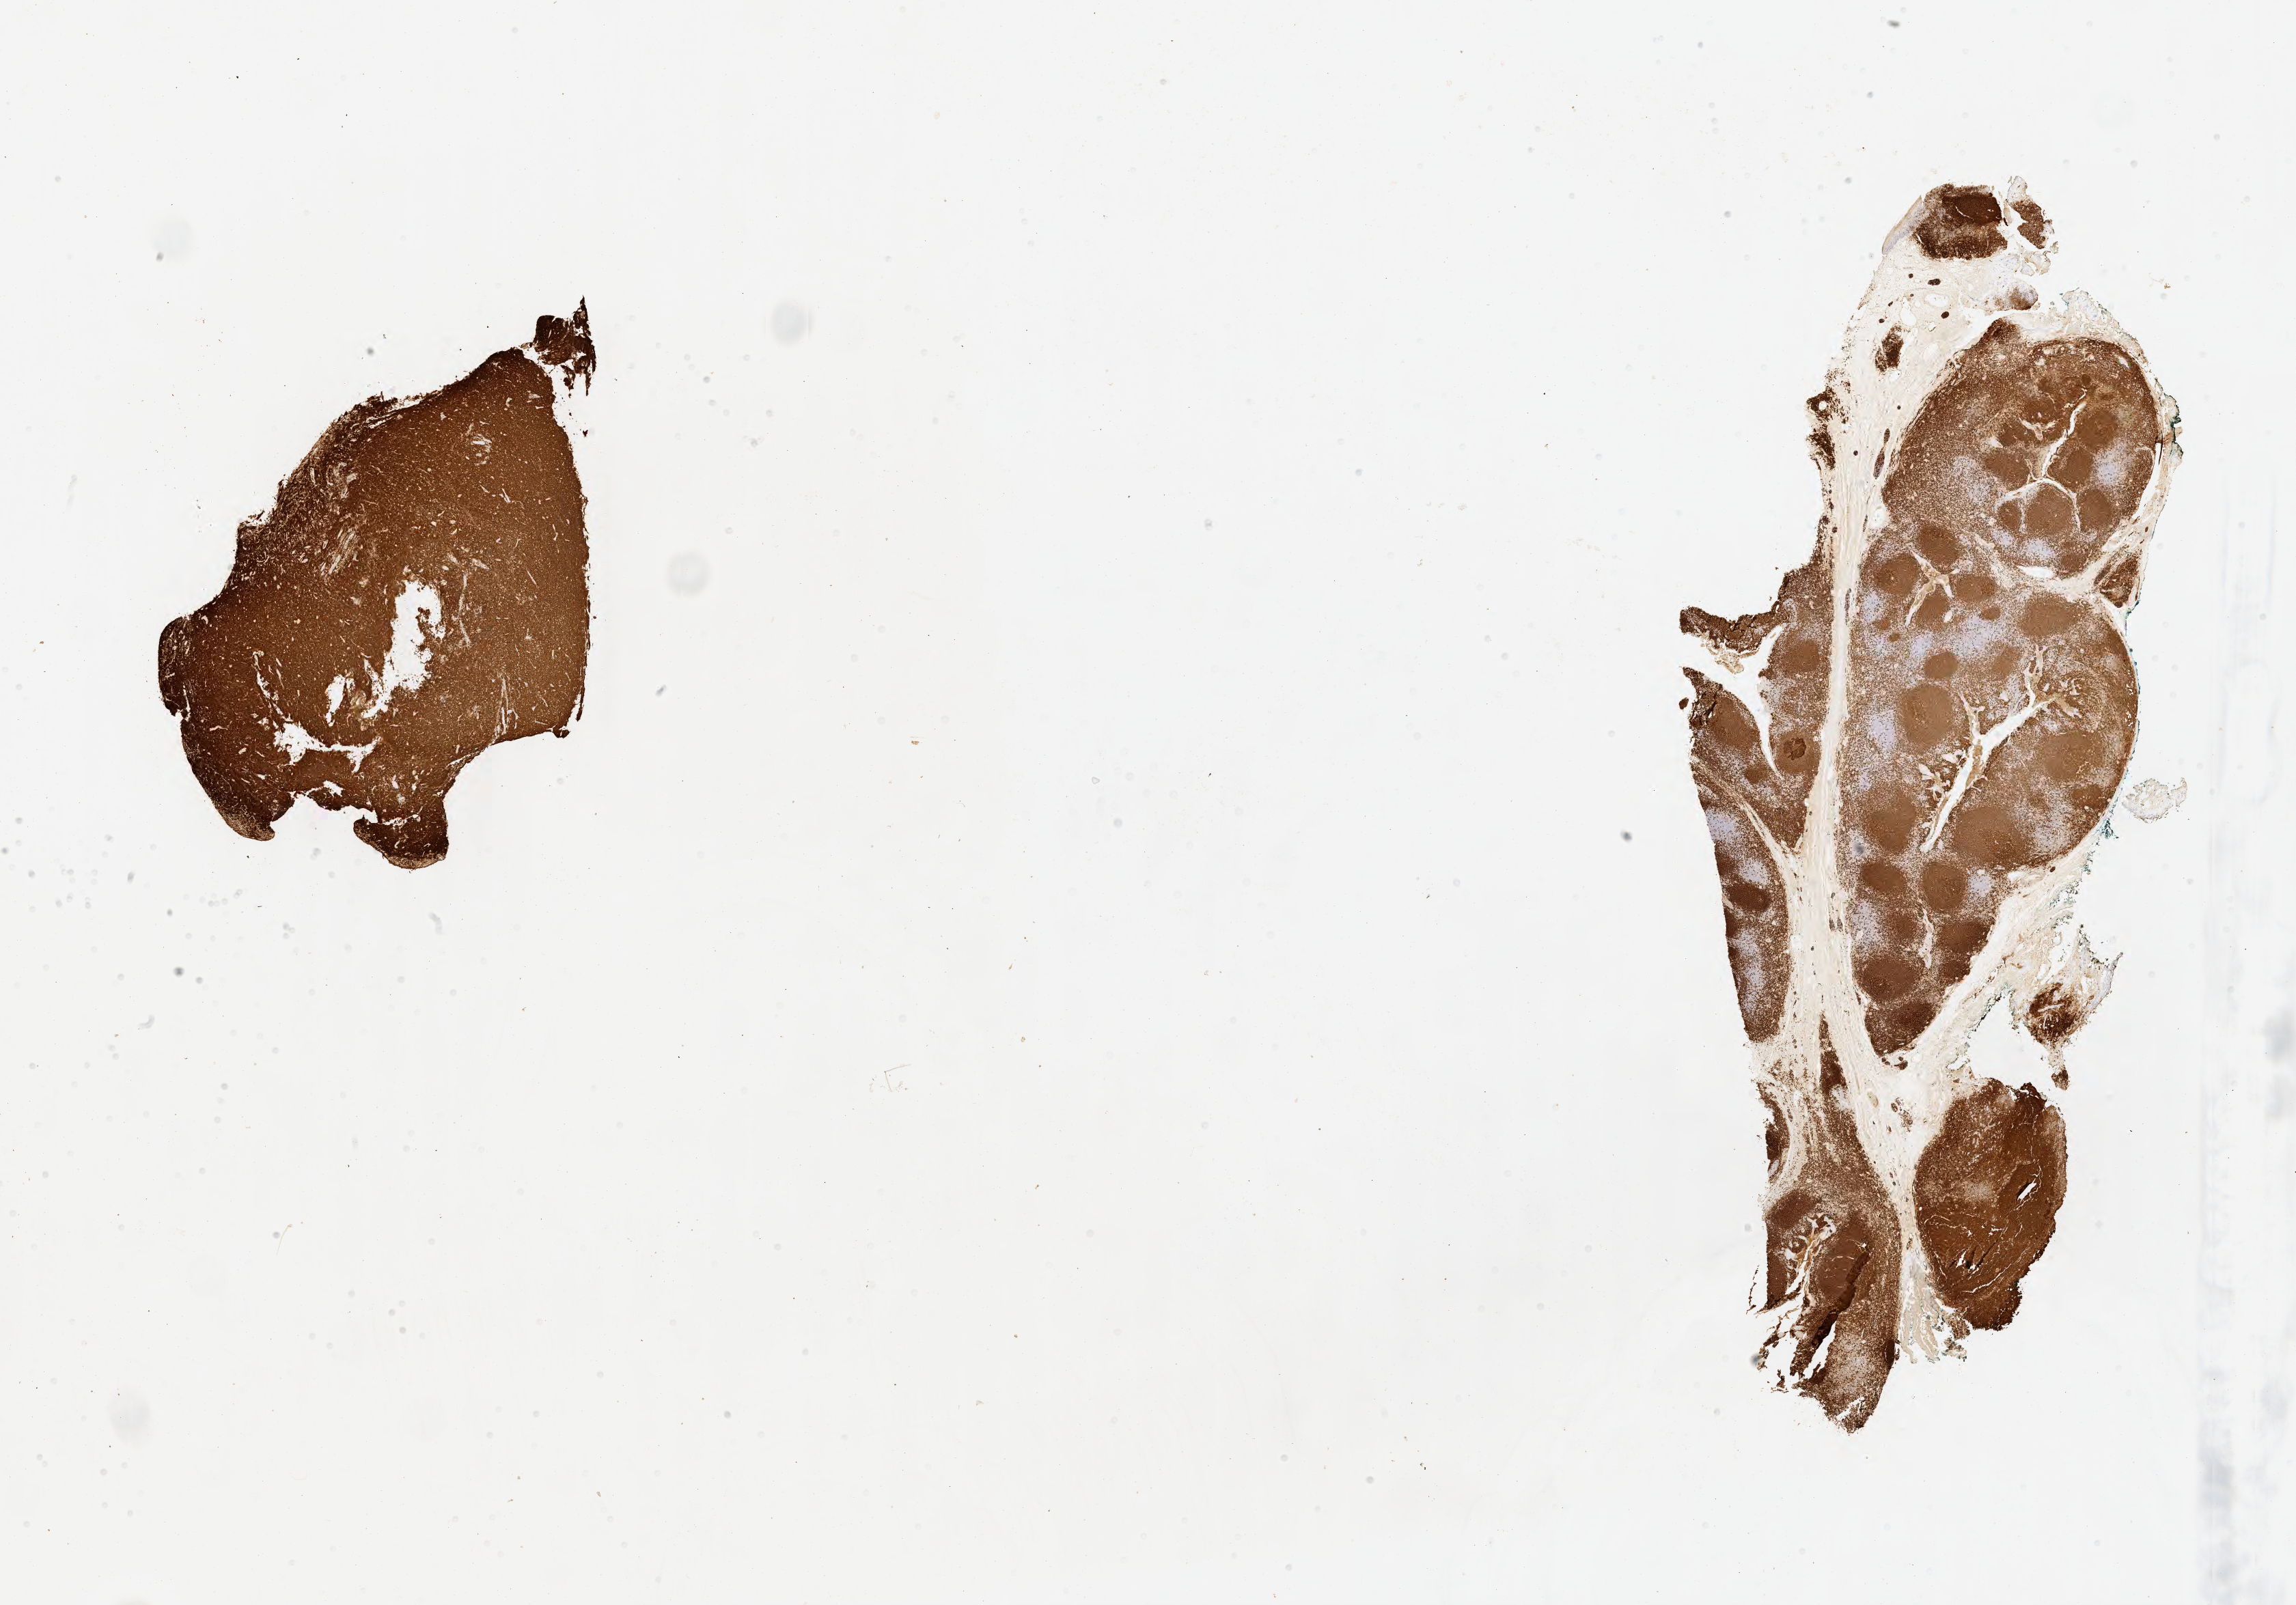
Immunohistochemistry (IHC) whole-slide image stained for CD20, shown as a low-resolution overview of the whole scanned area (about 27.2 x 19.0 mm). Specimen: tumor tissue. Anatomic site: ovary. Patient: female, age at initial diagnosis 3 years.
Histologic diagnosis: Burkitt lymphoma, NOS.